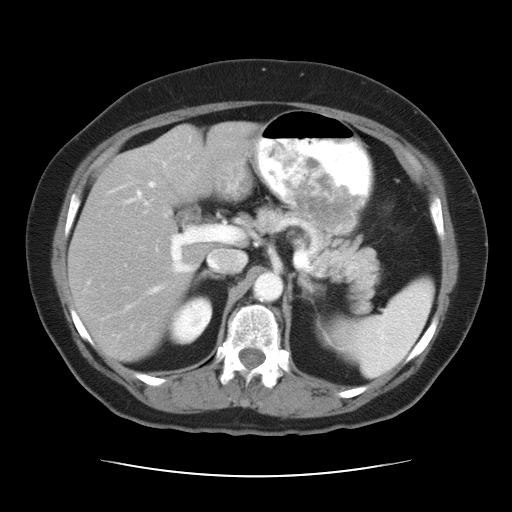
Contrast-enhanced abdominal CT, one axial slice. Position 19 of 34 along the scan axis. 120 kVp. Intravenous contrast given. Soft-tissue window (W 400 / L 40 HU). 512 × 512 image matrix. Female patient, age 65 years. From the clinical record (not read from this slice): diagnosis: colorectal cancer liver metastases, imaged before liver resection; multiple liver metastases: yes; largest metastasis: 2.2 cm; disease in both lobes: no.
Outlined on this slice (expert manual segmentation):
- hepatic veins: bounding box [x1, y1, x2, y2] px = [137, 181, 246, 271]
- liver: [69, 125, 249, 360]
- planned liver remnant (the part of the liver to remain after resection): [69, 125, 249, 360]
- portal vein (with intrahepatic branches): [123, 195, 228, 294]